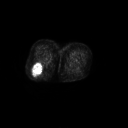
FDG PET of an extremity soft-tissue mass (from a PET/CT study), one axial slice; slice 30 of 267 in the series (ordered by position); 3.27 mm slice thickness; 128 × 128 image matrix, field of view 700 × 700 mm. Female patient, age 70 years. Case-level facts recorded for this patient, not image findings: histological type: synovial sarcoma; grade: intermediate; site of the primary tumour: right buttock.
Annotated regions visible in this slice (expert contour drawn on MRI and transferred to this co-registered scan by the dataset authors):
- gross tumour volume including surrounding oedema: box from (x=32, y=61) to (x=42, y=74) px
- gross tumour volume (mass): (x=32, y=63)–(x=42, y=74)